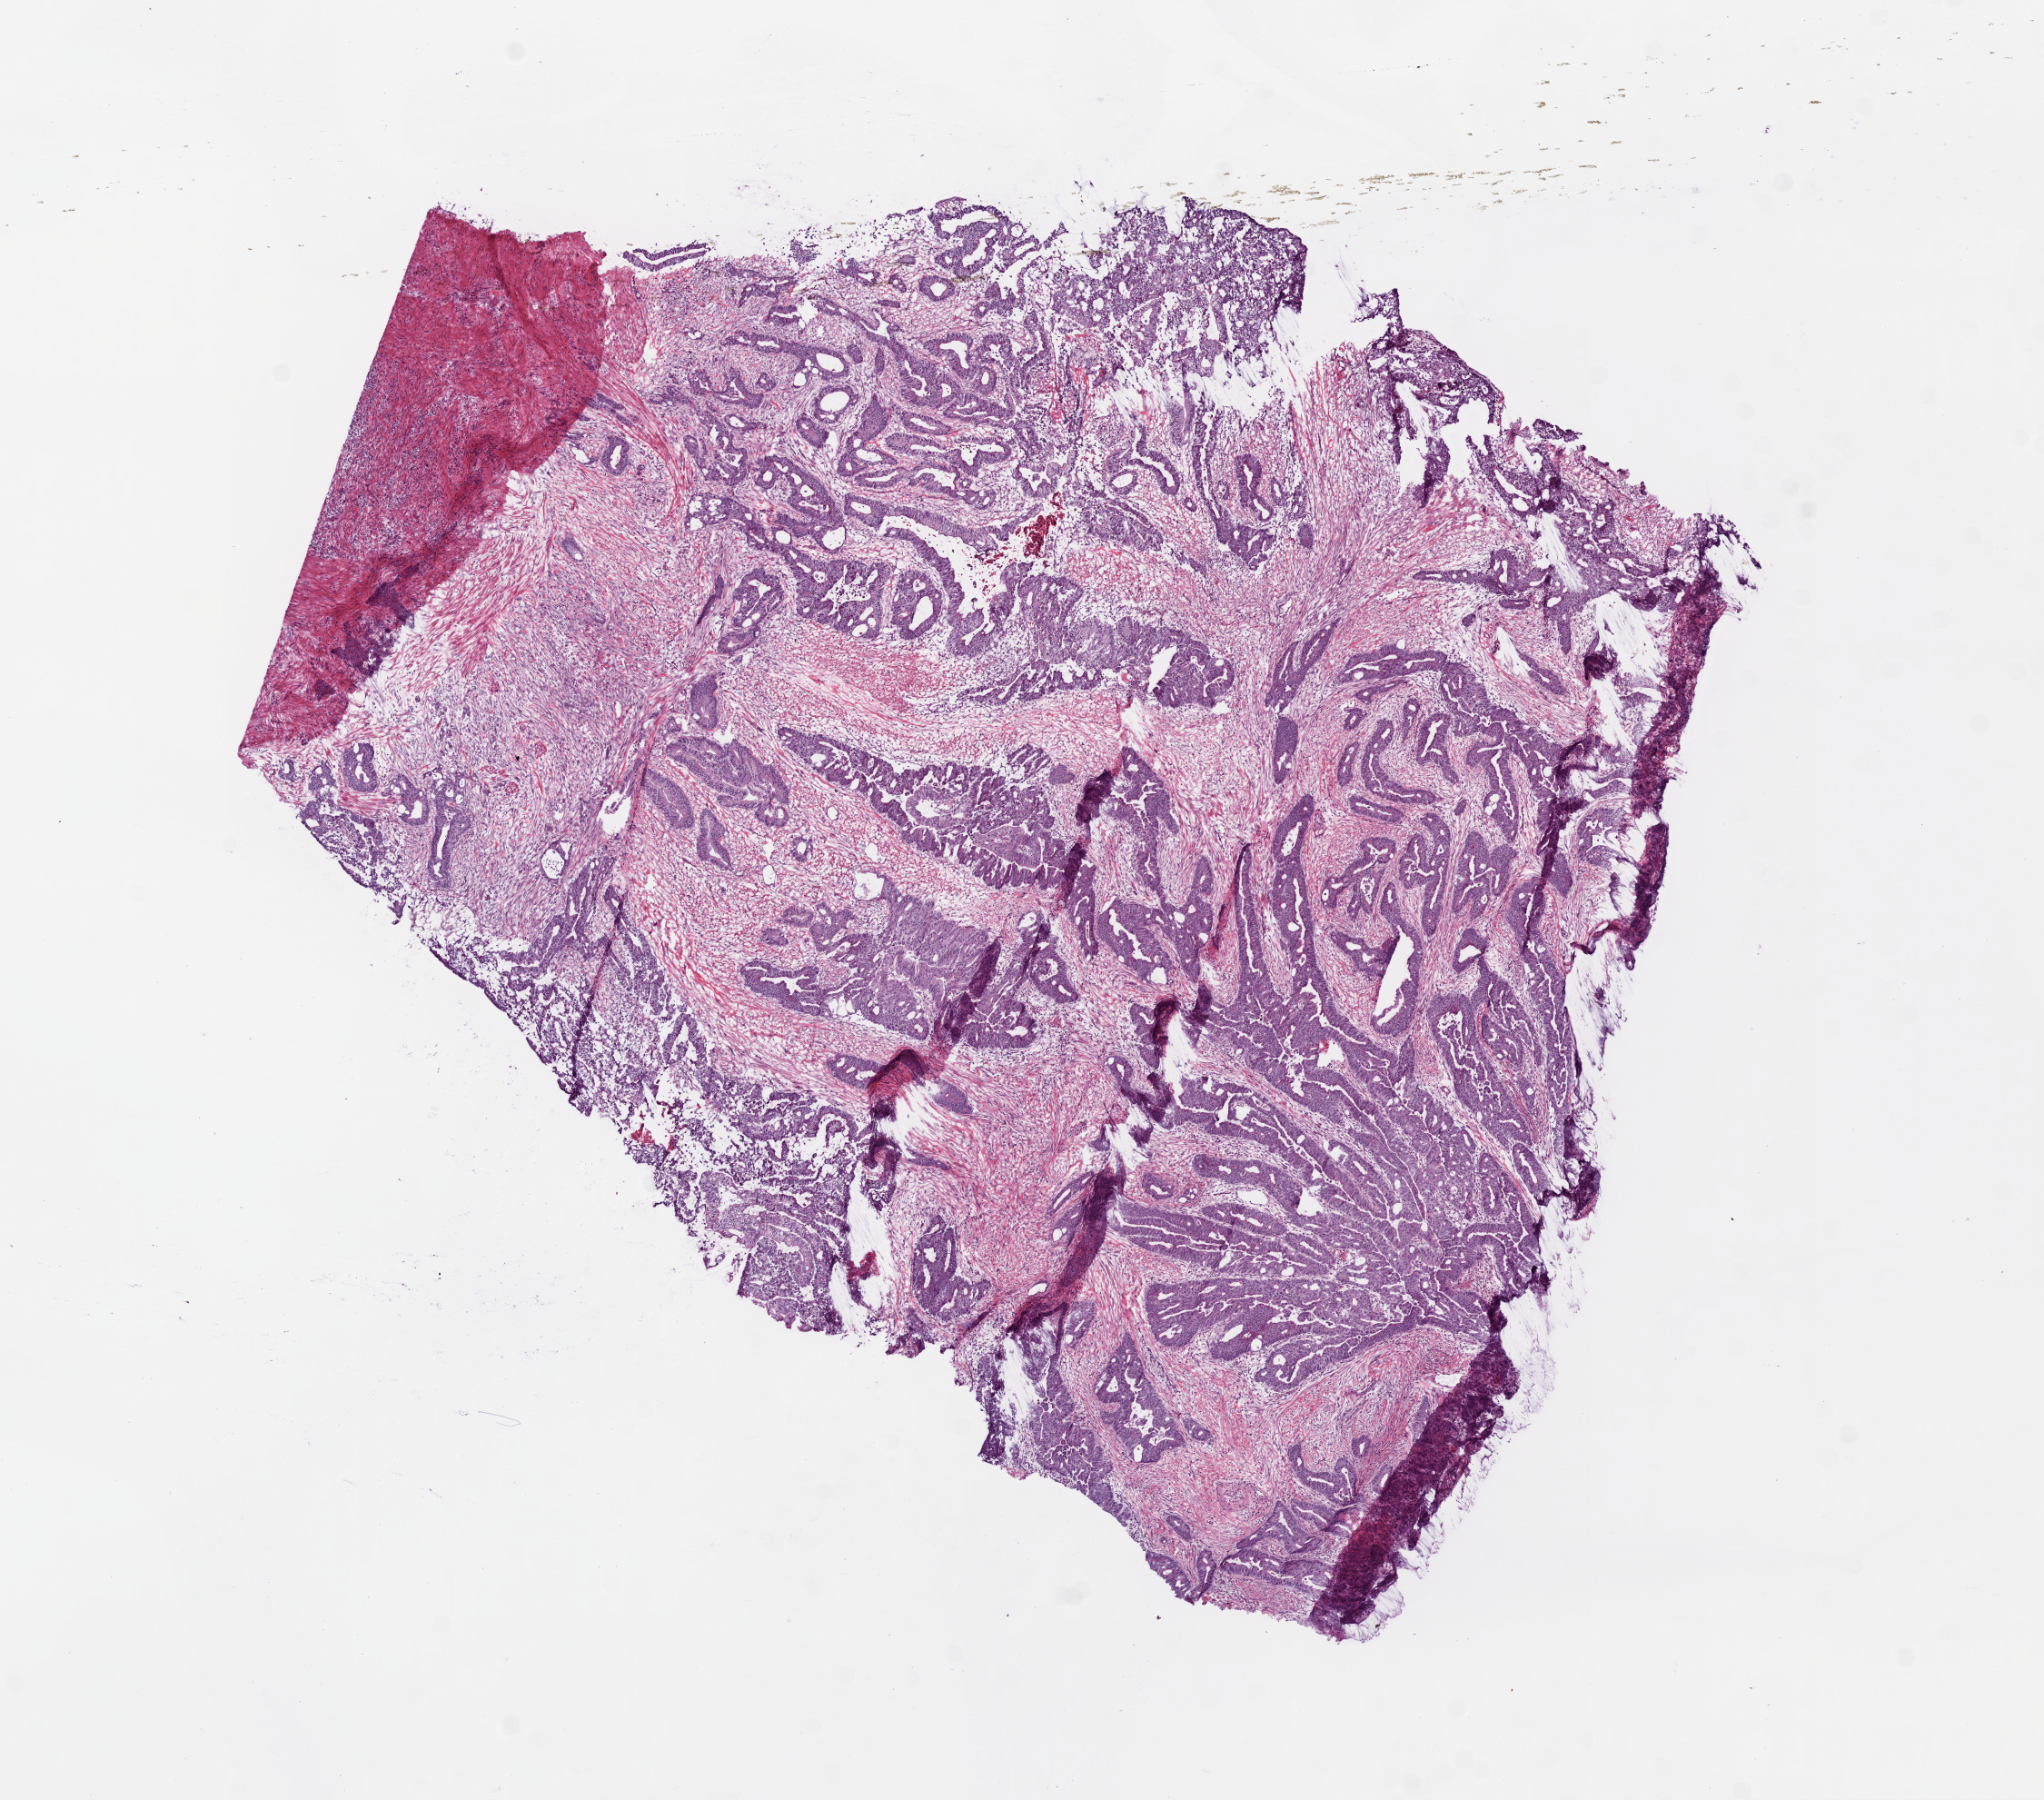
Digitized H&E tissue section (whole slide), whole scanned area (about 9.0 x 7.9 mm) shown as a low-resolution overview. Frozen section. Sample: primary tumour, rectum. Male, age 60 years at initial diagnosis. Composition of this section per pathologist review: tumour cells 75%, tumour nuclei 70%, normal cells 0%, stromal cells 20%, necrosis 5%.
AJCC pathologic stage: IV. TNM: T3 N1 M1. Histologic diagnosis: Adenocarcinoma, NOS (rectosigmoid junction).